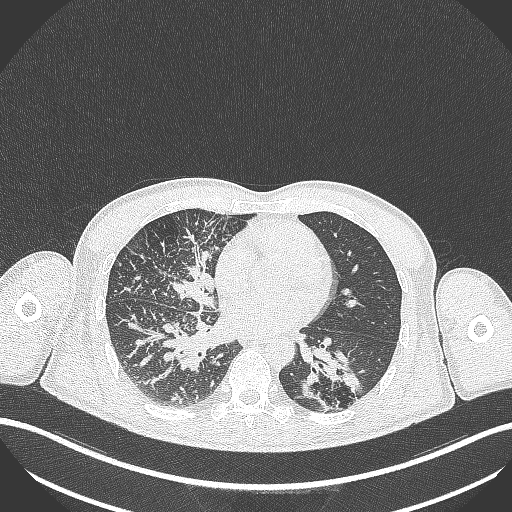
Chest CT, one axial slice; slice 138 of 348 in the series (ordered by position); lung window (W 1500 / L -600 HU); 1 mm slice thickness; 512 × 512 image matrix, field of view 400 × 400 mm. Male patient, age 49 years. From the clinical record (not read from this slice): clinical TNM (as recorded): T2b N1 M0.
Outlined on this slice (bounding box drawn by a radiologist):
- lung tumour (recorded histology: adenocarcinoma): bounding box (x1, y1, x2, y2) in pixels: (295, 337, 369, 414)